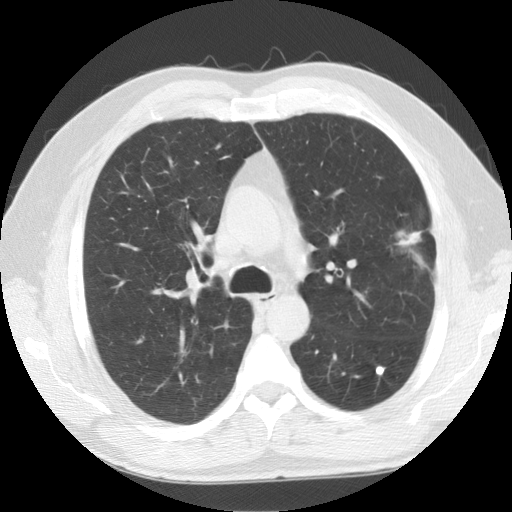
Low-dose screening chest CT, one axial slice; slice 97 of 141 in the series (ordered by position); reconstruction kernel STANDARD; 120 kVp; lung window (W 1500 / L -600 HU); 2.5 mm slice thickness; 512 × 512 image matrix.
Annotated regions visible in this slice (outlined manually by an expert reader):
- lesion 1 (tumor, upper lobe of left lung): bounding box [x1, y1, x2, y2] px = [397, 231, 423, 265]